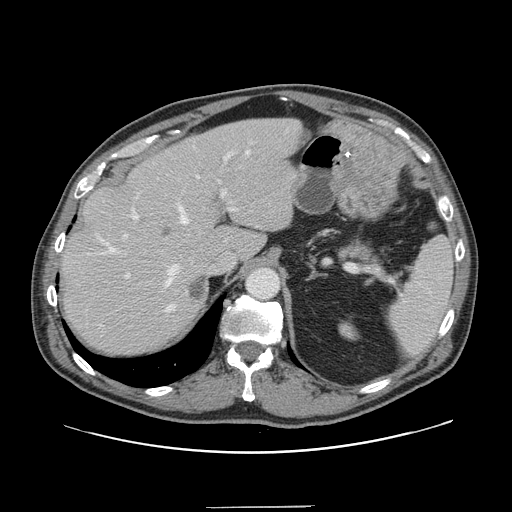
Contrast-enhanced abdominal CT, one axial slice; slice 107 of 139 in the series (ordered by position); soft-tissue window (W 400 / L 40 HU); 2.5 mm slice thickness; 512 × 512 image matrix. Male patient, age 64 years. Case-level facts recorded for this patient, not image findings: diagnosis: colorectal cancer liver metastases, imaged before liver resection; multiple liver metastases: yes.
Structures marked on this image (manually delineated by an expert):
- hepatic veins: bounding box <97,150,250,312> (left, top, right, bottom; pixels)
- liver: <62,119,300,353>
- planned liver remnant (the part of the liver to remain after resection): <61,120,273,353>
- portal vein (with intrahepatic branches): <123,152,236,278>
- liver metastasis: <187,275,208,305>